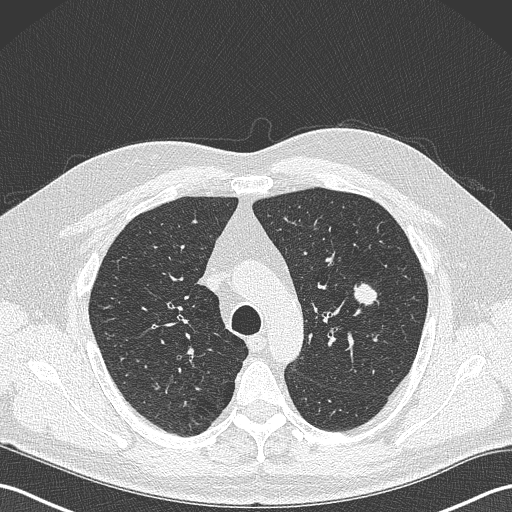
Chest CT (low-dose screening protocol), one axial image; baseline annual screen; lung window (W 1500 / L -600 HU); slice 95 of 343 in the series; 512 × 512 image matrix, field of view 350 × 350 mm. Male, age 61 years at enrolment. Former smoker at enrolment.
Expert-annotated lung lesion, bounding box (x1, y1, x2, y2) in pixels: (345, 278, 385, 314). The screening reader recorded 2 non-calcified nodules or masses ≥4 mm on this exam (left upper lobe, lingula); which of them this box marks is not recorded. Official screen result: positive, change unspecified: nodule(s) >= 4 mm or enlarging nodule(s), mass(es), or other non-specific abnormalities suspicious for lung cancer. Later outcome: lung cancer diagnosed 160 days after this screen — adenocarcinoma, NOS, left upper lobe, poorly differentiated (G3), stage IA (AJCC 6th edition), 28 mm at pathology.